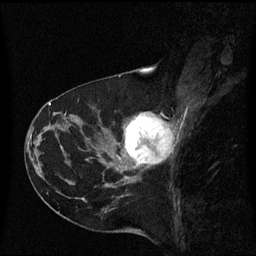
Breast MRI (dynamic contrast-enhanced), one sagittal slice. Slice 28 of 60 in the series (ordered by position). Dynamic contrast-enhanced series, image 2 of 3 at this slice position (ordered by acquisition). 1.5 T. TE 4.2 ms, TR 8.4 ms. 256 × 256 image matrix. Female patient, age 41 years. Case-level facts recorded for this patient, not image findings: setting: breast cancer imaged before/during neoadjuvant chemotherapy; receptor status: triple-negative.
Structures marked on this image (semi-automatic segmentation, software-assisted and operator-edited):
- analysis volume of interest (the breast-tissue region the enhancement analysis was run in; not a lesion): bounding box (x1, y1, x2, y2) in pixels: (116, 114, 175, 177)
- tumour enhancement mask (voxels above the 70 % enhancement threshold inside the analysis volume of interest): (124, 114, 172, 167)